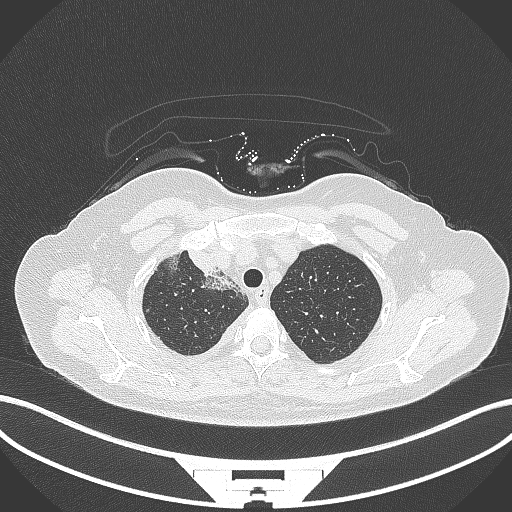
Chest CT, one axial slice; reconstruction kernel B70f; lung window (W 1500 / L -600 HU); 1 mm slice thickness; 512 × 512 image matrix. Female patient, age 52 years. From the clinical record (not read from this slice): clinical TNM (as recorded): T3 N1 M1.
Structures marked on this image (rectangle marked by the reading radiologist):
- lung tumour (recorded histology: adenocarcinoma): bounding box (x1, y1, x2, y2) in pixels: (180, 244, 223, 280)